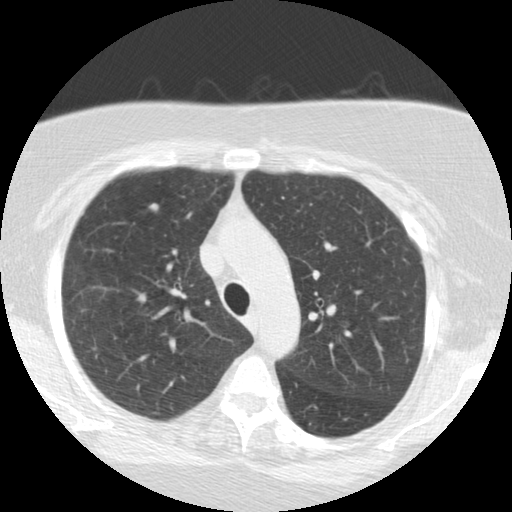
Low-dose screening chest CT, one axial slice; position 172 of 225 along the scan axis; lung window (W 1500 / L -600 HU); 512 × 512 image matrix, field of view 320 × 320 mm.
Outlined on this slice (manually delineated by an expert):
- lesion 1 (tumor, upper lobe of right lung): bounding box (x1, y1, x2, y2) in pixels: (149, 203, 159, 211)